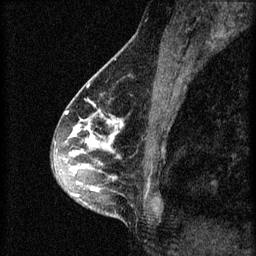
Breast MRI (dynamic contrast-enhanced), one sagittal slice. Slice 28 of 60 in the series (ordered by position). 3 images stored at this slice position (order not interpretable as contrast timing). 1.5 T. TE 4.2 ms, TR 8.2 ms. 256 × 256 image matrix, field of view 180 × 180 mm. Patient: female, 45 years.
Outlined on this slice (semi-automatically segmented with operator editing):
- analysis volume of interest (the breast-tissue region the enhancement analysis was run in; not a lesion): bounding box [x1, y1, x2, y2] px = [54, 104, 159, 217]
- tumour enhancement mask (voxels above the 70 % enhancement threshold inside the analysis volume of interest): [54, 110, 123, 197]